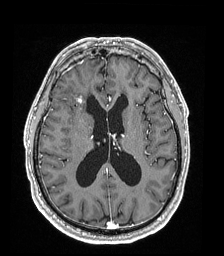
Brain MRI from a brain-tumour surgery series, one axial slice. Position 85 of 192 along the scan axis. T1-weighted post-contrast. 1 mm slice thickness. 224 × 256 image matrix, field of view 224 × 256 mm. Case-level facts recorded for this patient, not image findings: histopathology: Astrocytoma; WHO grade: 4.
Annotated regions visible in this slice (outlined manually by an expert reader):
- tumour: box from (x=77, y=98) to (x=82, y=103) px